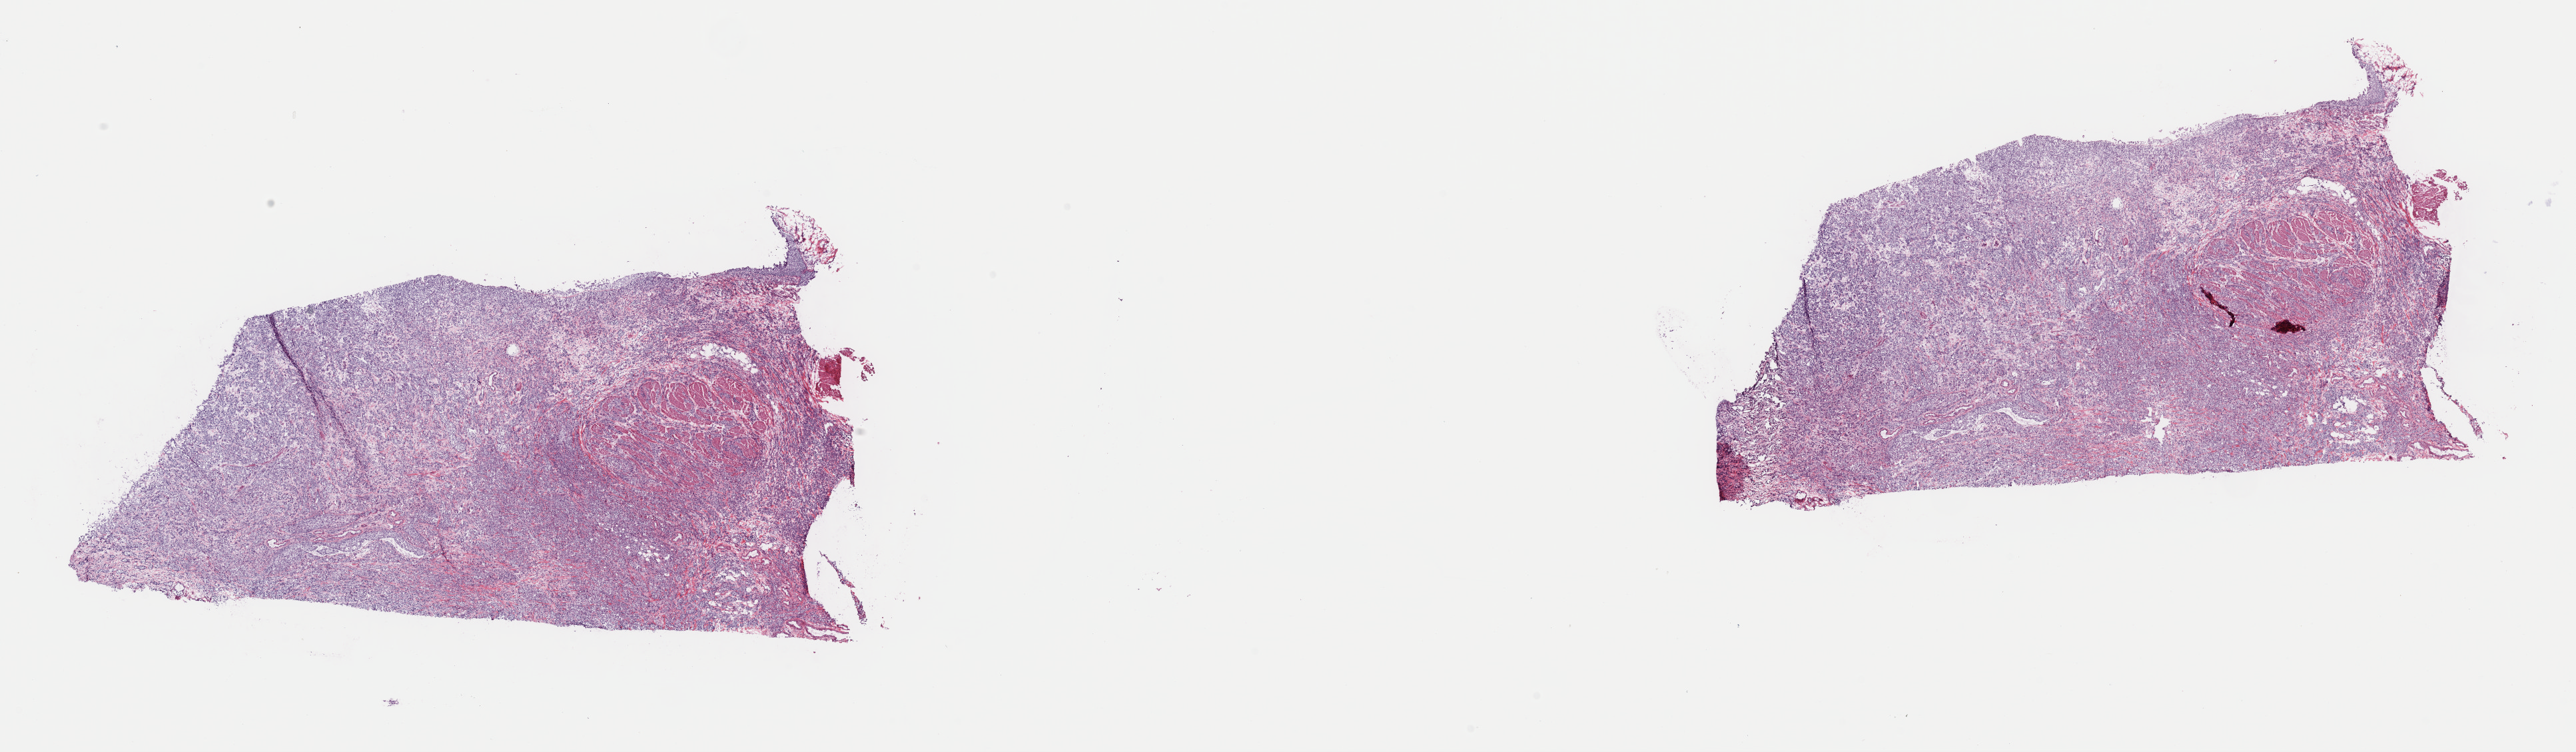
Digitized H&E tissue section (whole slide), low-resolution overview of the scanned area, about 30.5 x 8.9 mm; frozen section from the top of the tissue portion; primary tumour sample from the bladder. Patient: male, age at initial diagnosis 73 years. Histologic grade: high grade. Composition of this section per pathologist review: tumour cells 80%, tumour nuclei 85%, normal cells 0%, stromal cells 20%, necrosis 0%. Inflammatory infiltration, as recorded: lymphocyte infiltration 0%, monocyte infiltration 0%, neutrophil infiltration 0%.
Diagnosis: Transitional cell carcinoma. AJCC pathologic stage: IV (7th edition). Lymph nodes positive (case pathology): 1 of 21 examined.